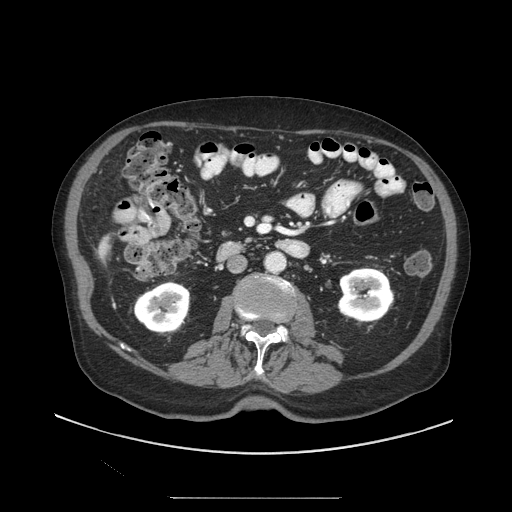
Contrast-enhanced abdominal CT (liver protocol), one axial slice; position 28 of 97 along the scan axis; reconstruction kernel STANDARD; 140 kVp; soft-tissue window (W 400 / L 40 HU); 512 × 512 image matrix. Case-level facts recorded for this patient, not image findings: diagnosis: hepatocellular carcinoma (patient treated with transarterial chemoembolisation; whether this scan precedes or follows treatment is not stated here); TNM stage (as recorded): Stage-IIIC; Child-Pugh class: A.
Annotated regions visible in this slice (semi-automatically segmented with operator editing):
- liver parenchyma outside the tumour (the mass and vessels are separate outlines, so this box may not span the whole liver): bounding box <98,236,110,261> (left, top, right, bottom; pixels)